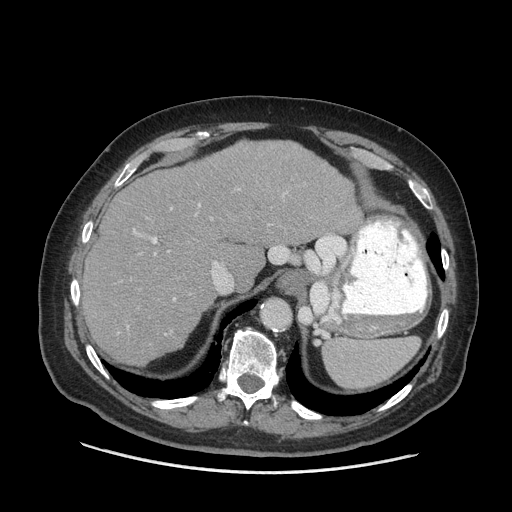
Contrast-enhanced abdominal CT (liver protocol), one axial slice; 140 kVp; soft-tissue window (W 400 / L 40 HU); 2.5 mm slice thickness; 512 × 512 image matrix, field of view 420 × 420 mm. From the clinical record (not read from this slice): diagnosis: hepatocellular carcinoma (patient treated with transarterial chemoembolisation; whether this scan precedes or follows treatment is not stated here); TNM stage (as recorded): Stage-I; Child-Pugh class: A.
Outlined on this slice (semi-automatic segmentation, software-assisted and operator-edited):
- liver parenchyma outside the tumour (the mass and vessels are separate outlines, so this box may not span the whole liver): box from (x=82, y=140) to (x=362, y=364) px
- liver vessels: (x=133, y=189)–(x=240, y=301)